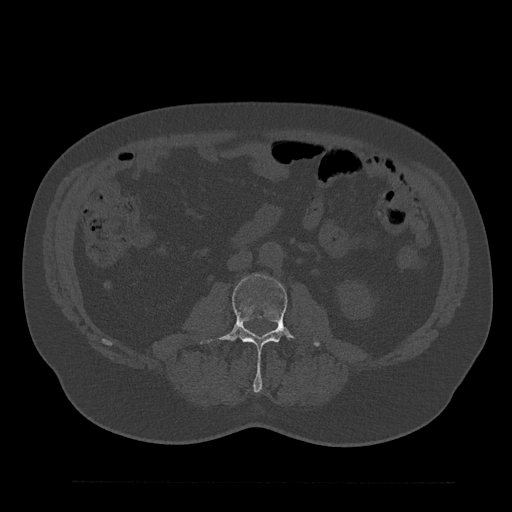
CT including the spine, one axial slice; position 33 of 797 along the scan axis; reconstruction kernel Br40s/3; 120 kVp; bone window (W 1800 / L 400 HU); 512 × 512 image matrix, field of view 430 × 430 mm. Male patient, age 61 years. Case-level facts recorded for this patient, not image findings: primary cancer: prostate.
Structures marked on this image (semi-automatic segmentation, software-assisted and operator-edited):
- L3 vertebra: bounding box <199,274,320,392> (left, top, right, bottom; pixels)